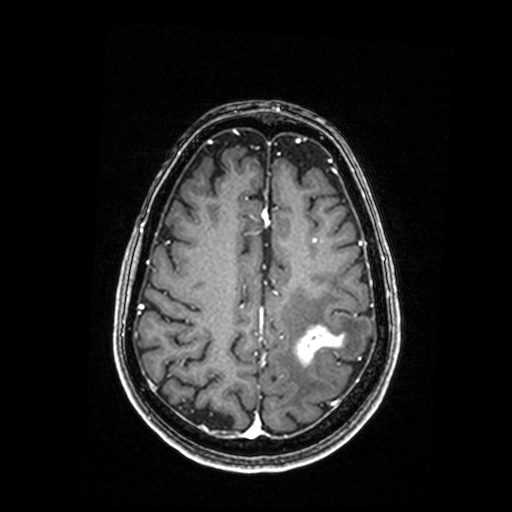
Brain MRI from a brain-tumour surgery series, one axial slice. Slice 61 of 192 in the series (ordered by position). T1-weighted post-contrast. 0.98 mm slice thickness. 512 × 512 image matrix, field of view 250 × 250 mm. From the clinical record (not read from this slice): histopathology: Metastastic Carcinoma, Poorly Differentiated; tumour location: Left Parietal.
Structures marked on this image (manually delineated by an expert):
- tumour: box from (x=295, y=327) to (x=344, y=366) px